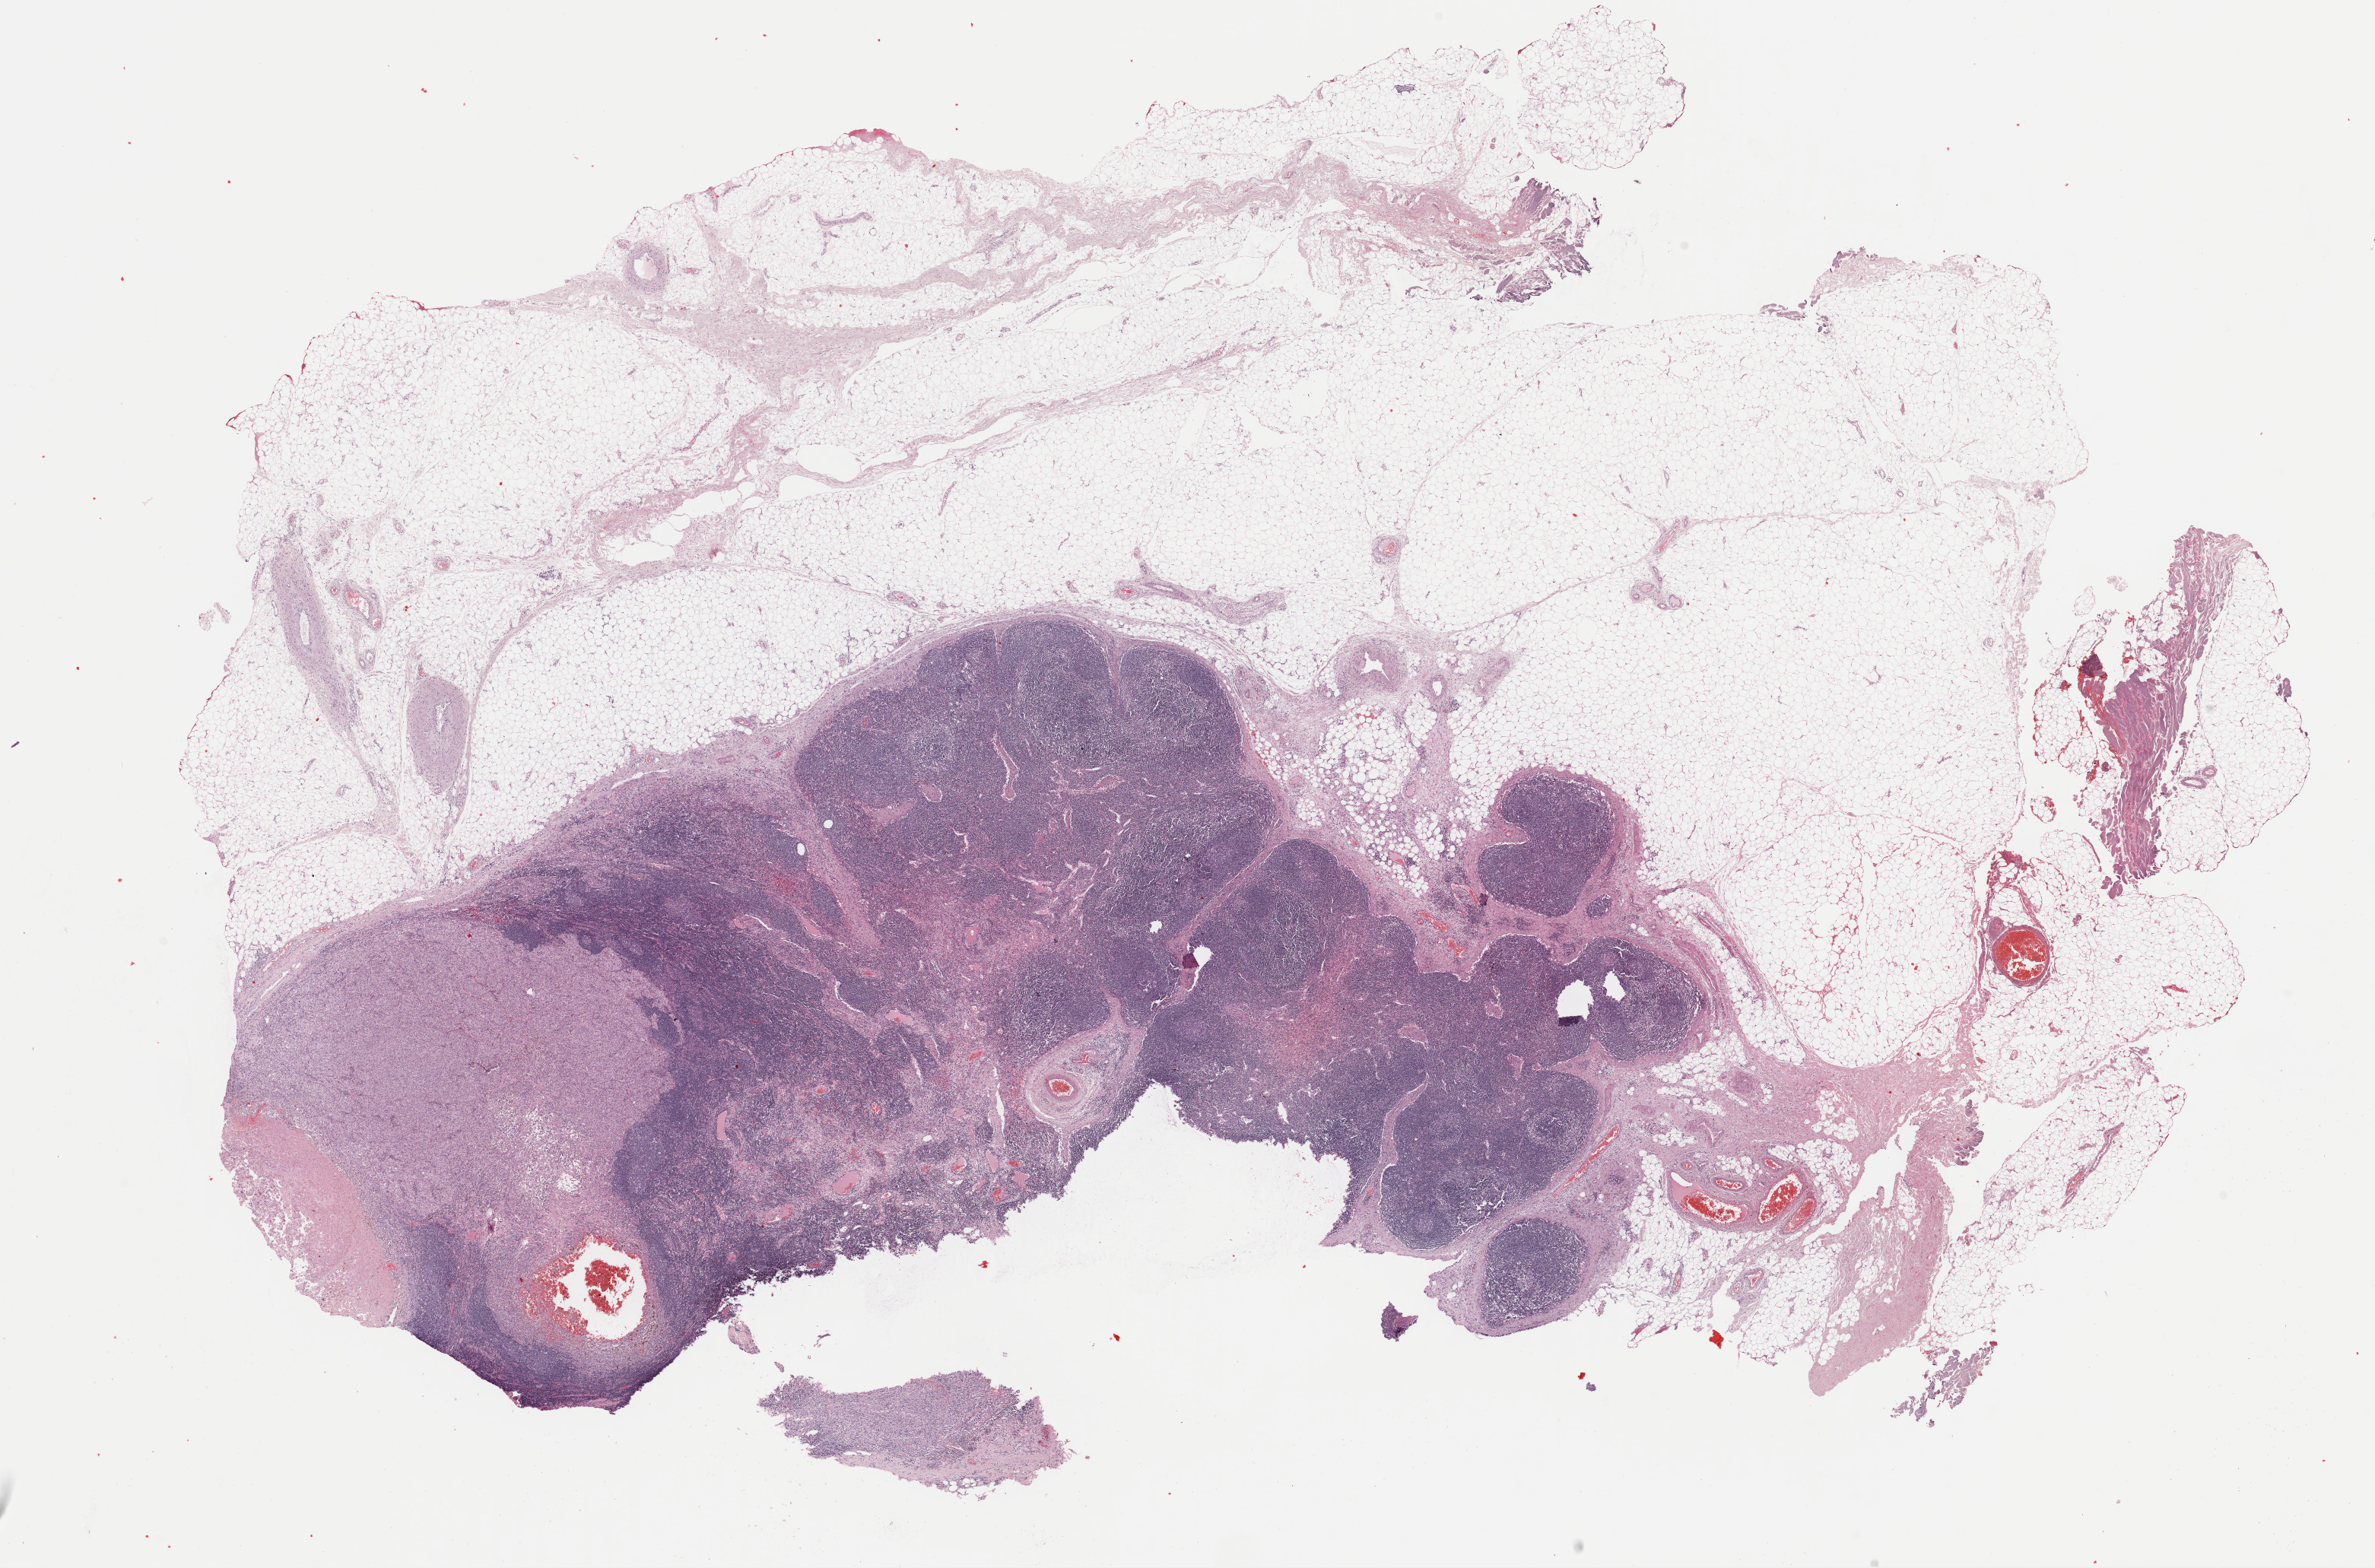
Hematoxylin and eosin (H&E) stained whole-slide image, a low-resolution overview of the entire scanned area, about 24.7 x 16.3 mm, FFPE section, metastatic tumour sample, sampled site: lymph nodes of axilla or arm. Female patient; age at initial diagnosis 39 years.
This section: metastatic tumour tissue. Patient diagnosis: Malignant melanoma, NOS.